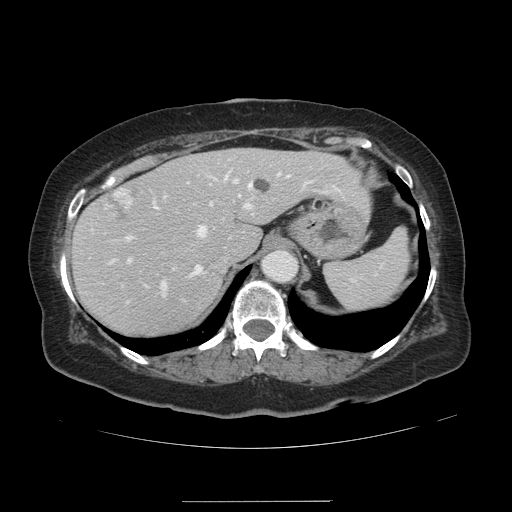
Contrast-enhanced abdominal CT, one axial slice; position 97 of 141 along the scan axis; 120 kVp; soft-tissue window (W 400 / L 40 HU); 2.5 mm slice thickness; 512 × 512 image matrix, field of view 393 × 393 mm. Female patient, age 74 years. From the clinical record (not read from this slice): diagnosis: colorectal cancer liver metastases, imaged before liver resection; multiple liver metastases: yes; largest metastasis: 7 cm; disease in both lobes: yes.
Outlined on this slice (manually delineated by an expert):
- hepatic veins: box from (x=153, y=173) to (x=280, y=277) px
- liver: (x=74, y=148)–(x=368, y=338)
- planned liver remnant (the part of the liver to remain after resection): (x=74, y=148)–(x=368, y=338)
- portal vein (with intrahepatic branches): (x=126, y=175)–(x=328, y=295)
- liver metastasis: (x=252, y=178)–(x=272, y=194)
- liver metastasis: (x=101, y=187)–(x=138, y=226)